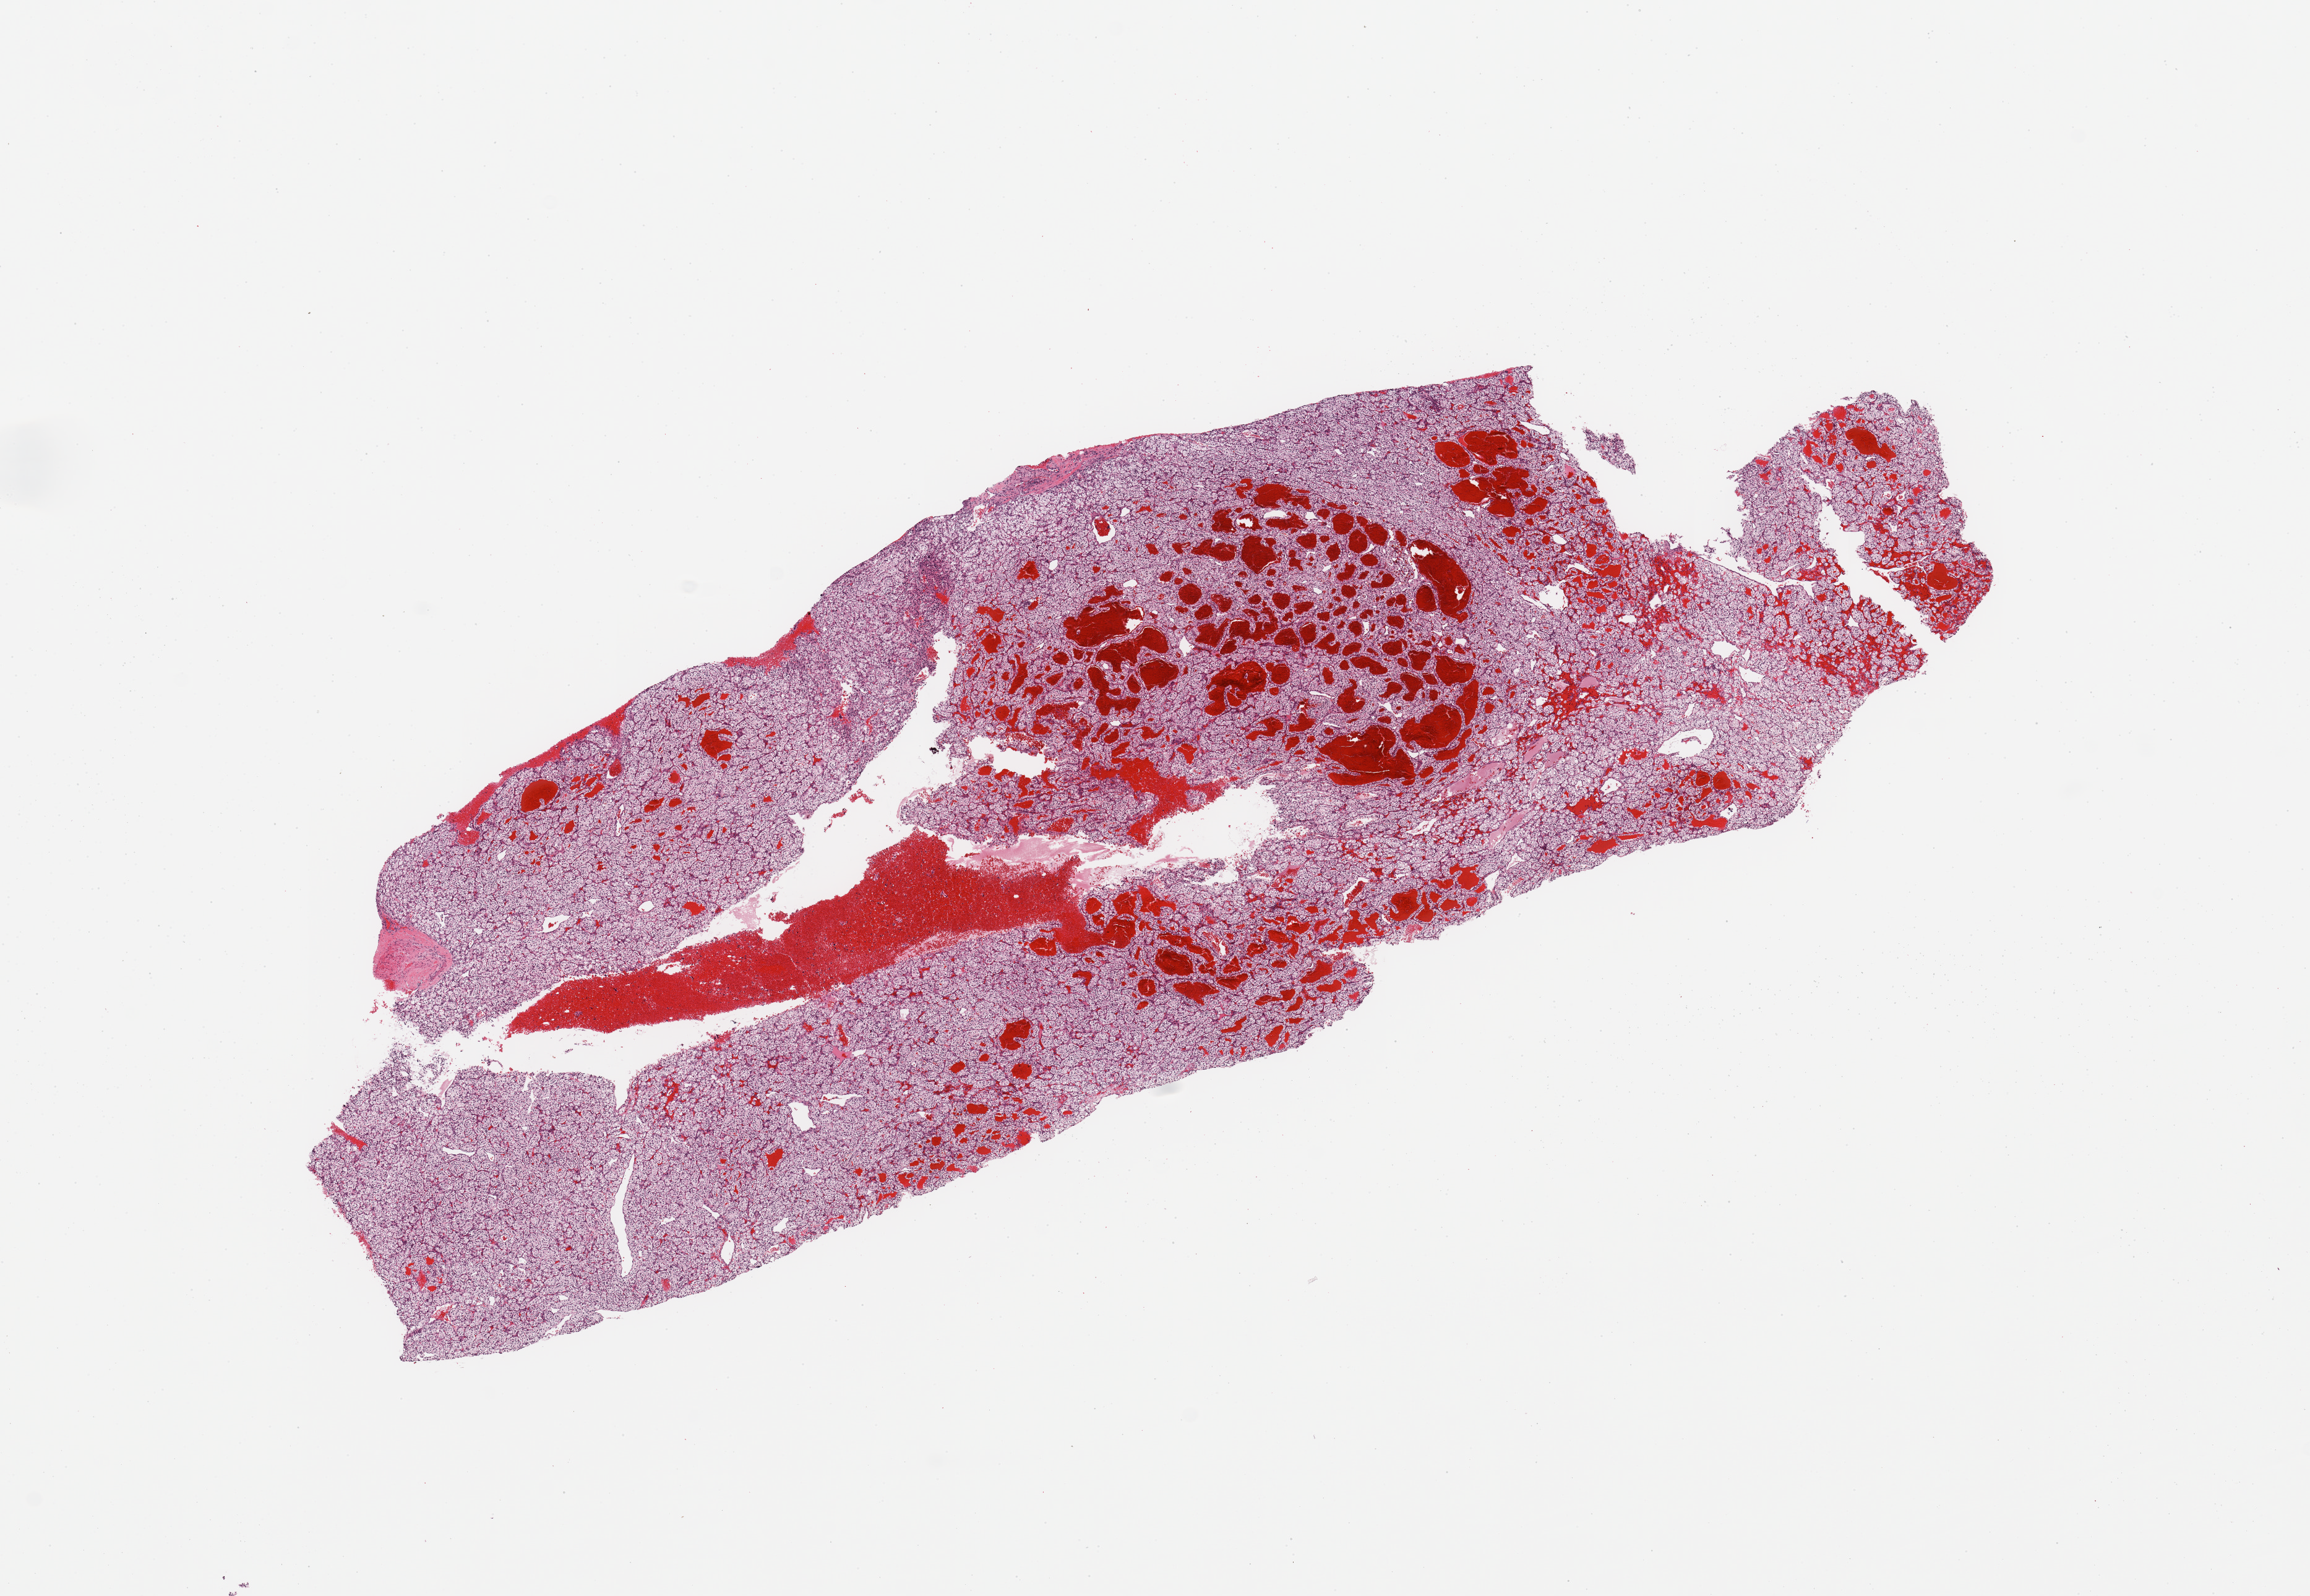
Hematoxylin and eosin (H&E) stained whole-slide image, whole scanned area (about 14.8 x 10.2 mm) shown as a low-resolution overview; tumour tissue sample, kidney. Female, 54 y/o. Histologic grade: G2 (moderately differentiated).
• diagnosis: Renal cell carcinoma, NOS
• AJCC pathologic stage: III